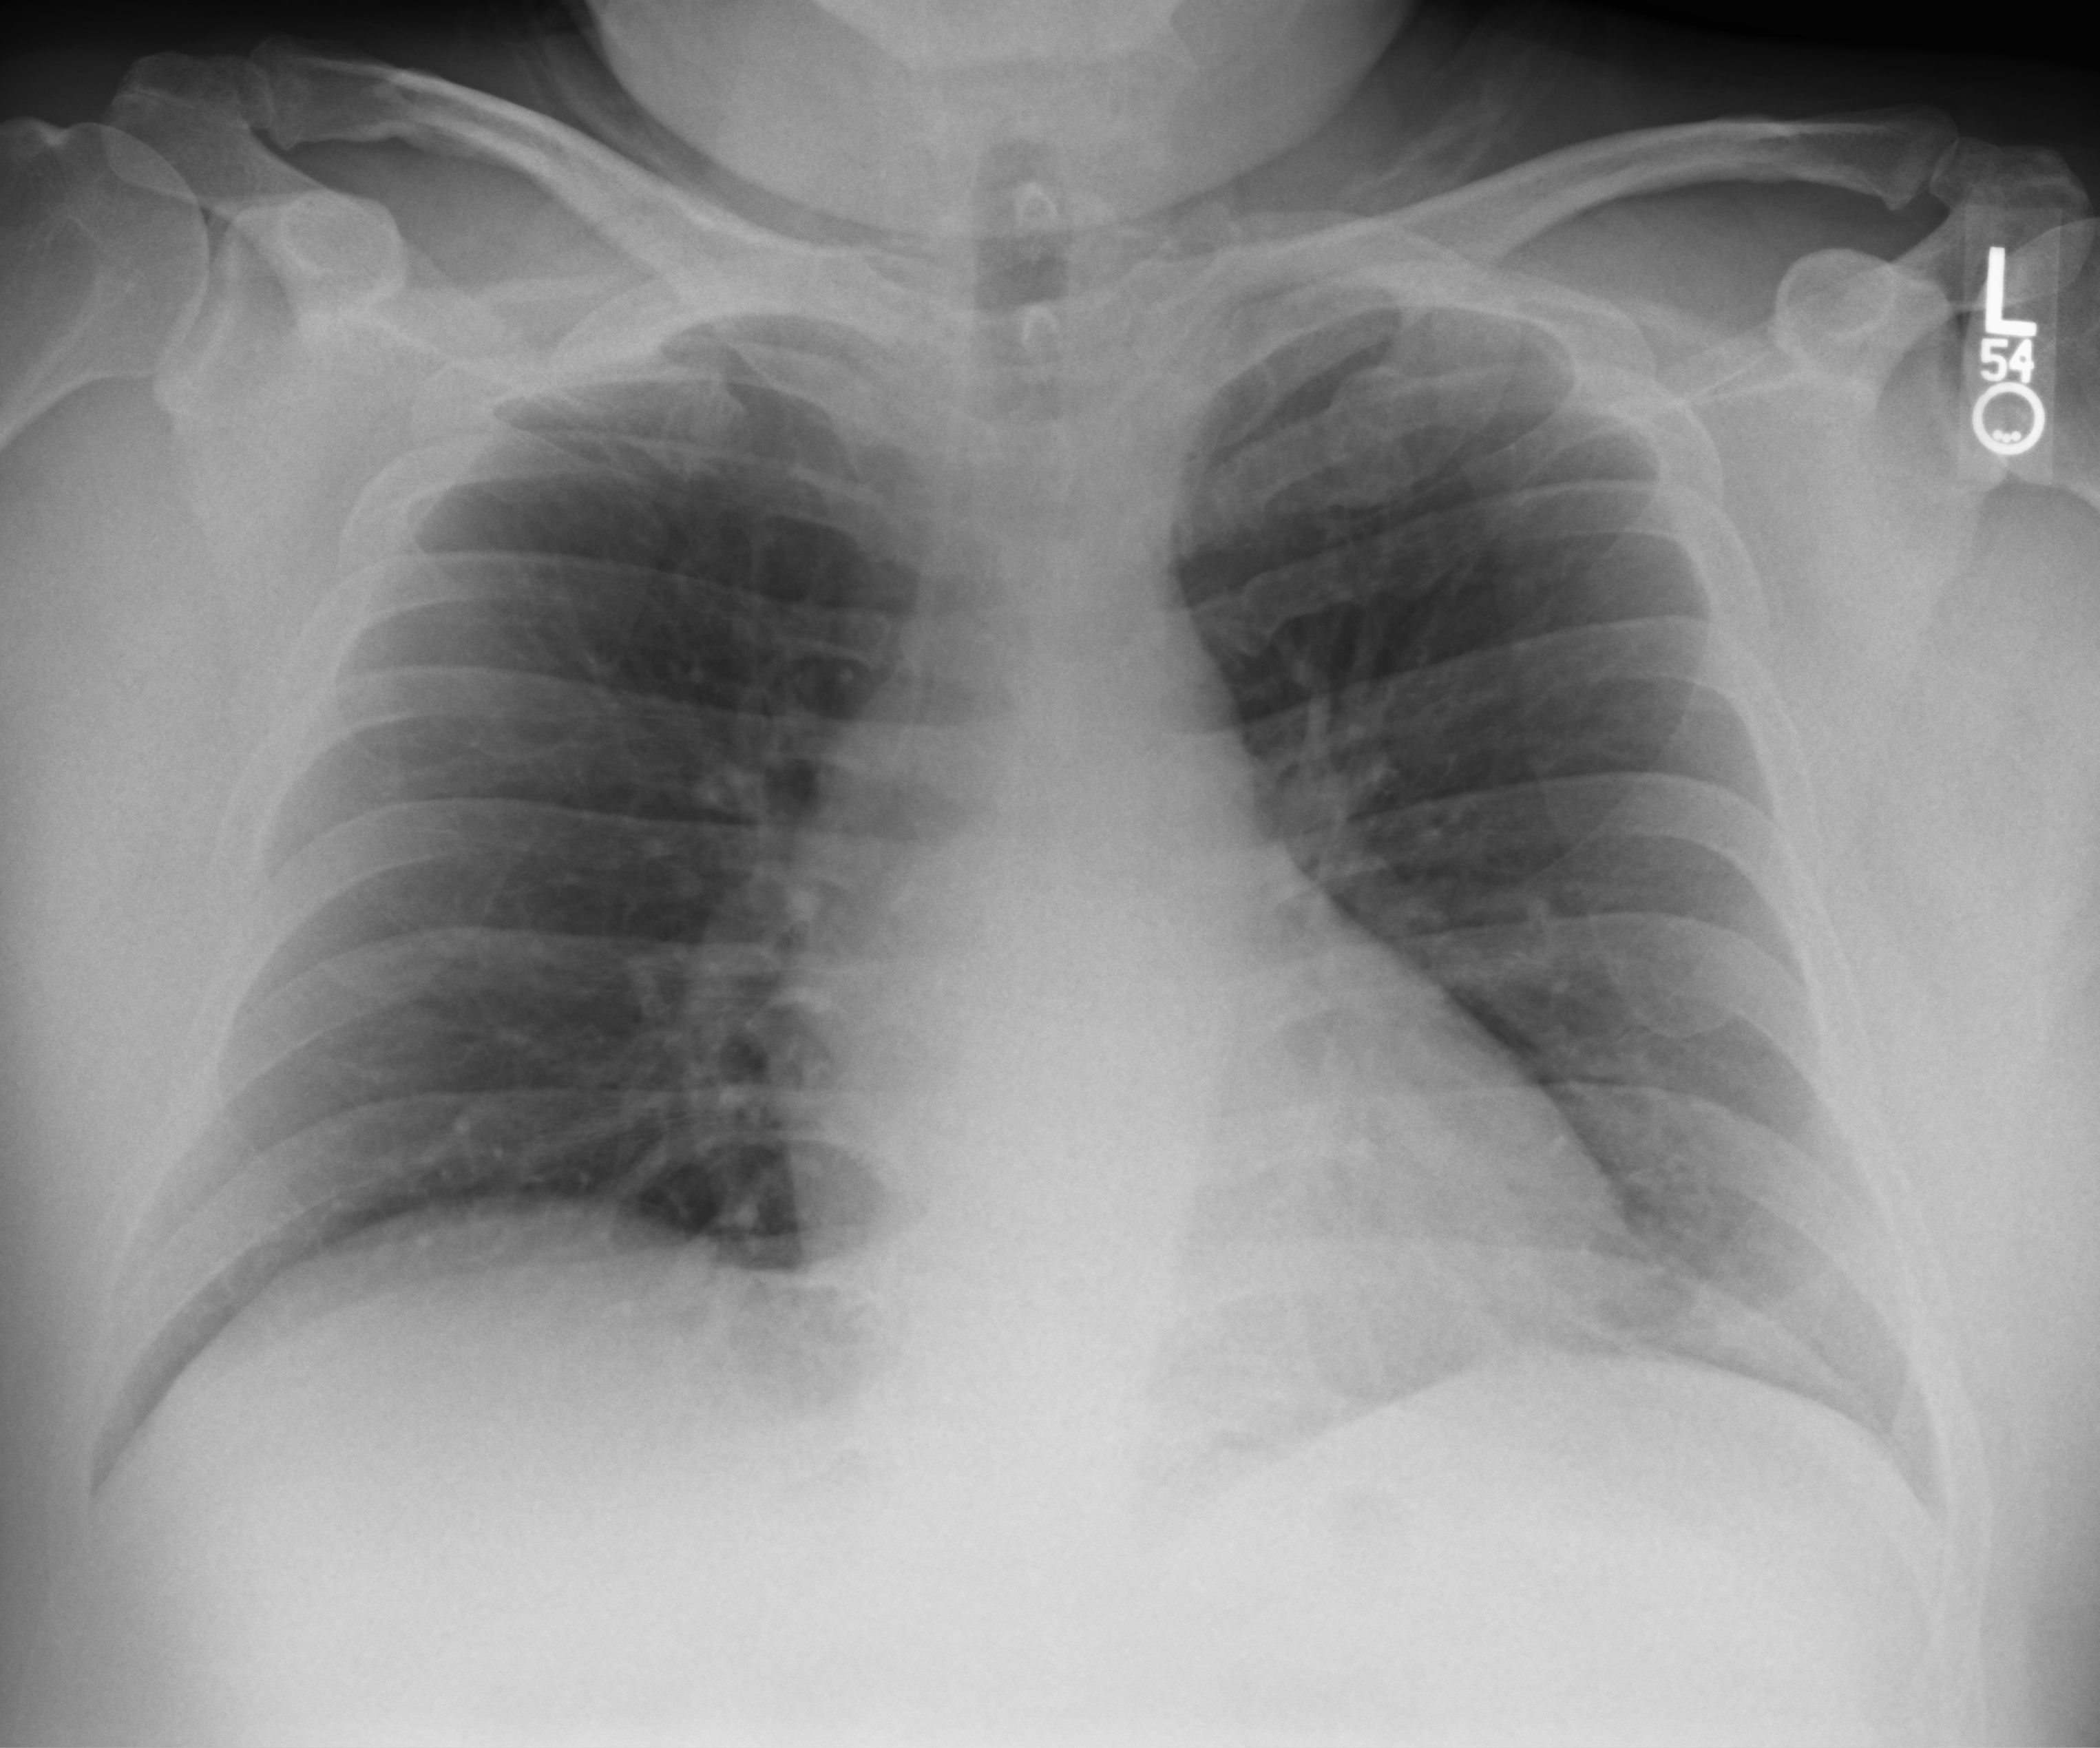
Chest X-ray (portable); anteroposterior (AP) projection. Male patient hospitalised with COVID-19, age 18–59 years.
Hospital-stay facts (about this admission, not read from this image; timing relative to this image not recorded): hypertension (admission record): yes; admitted to intensive care during this hospital stay: no; length of hospital stay: 1 day.